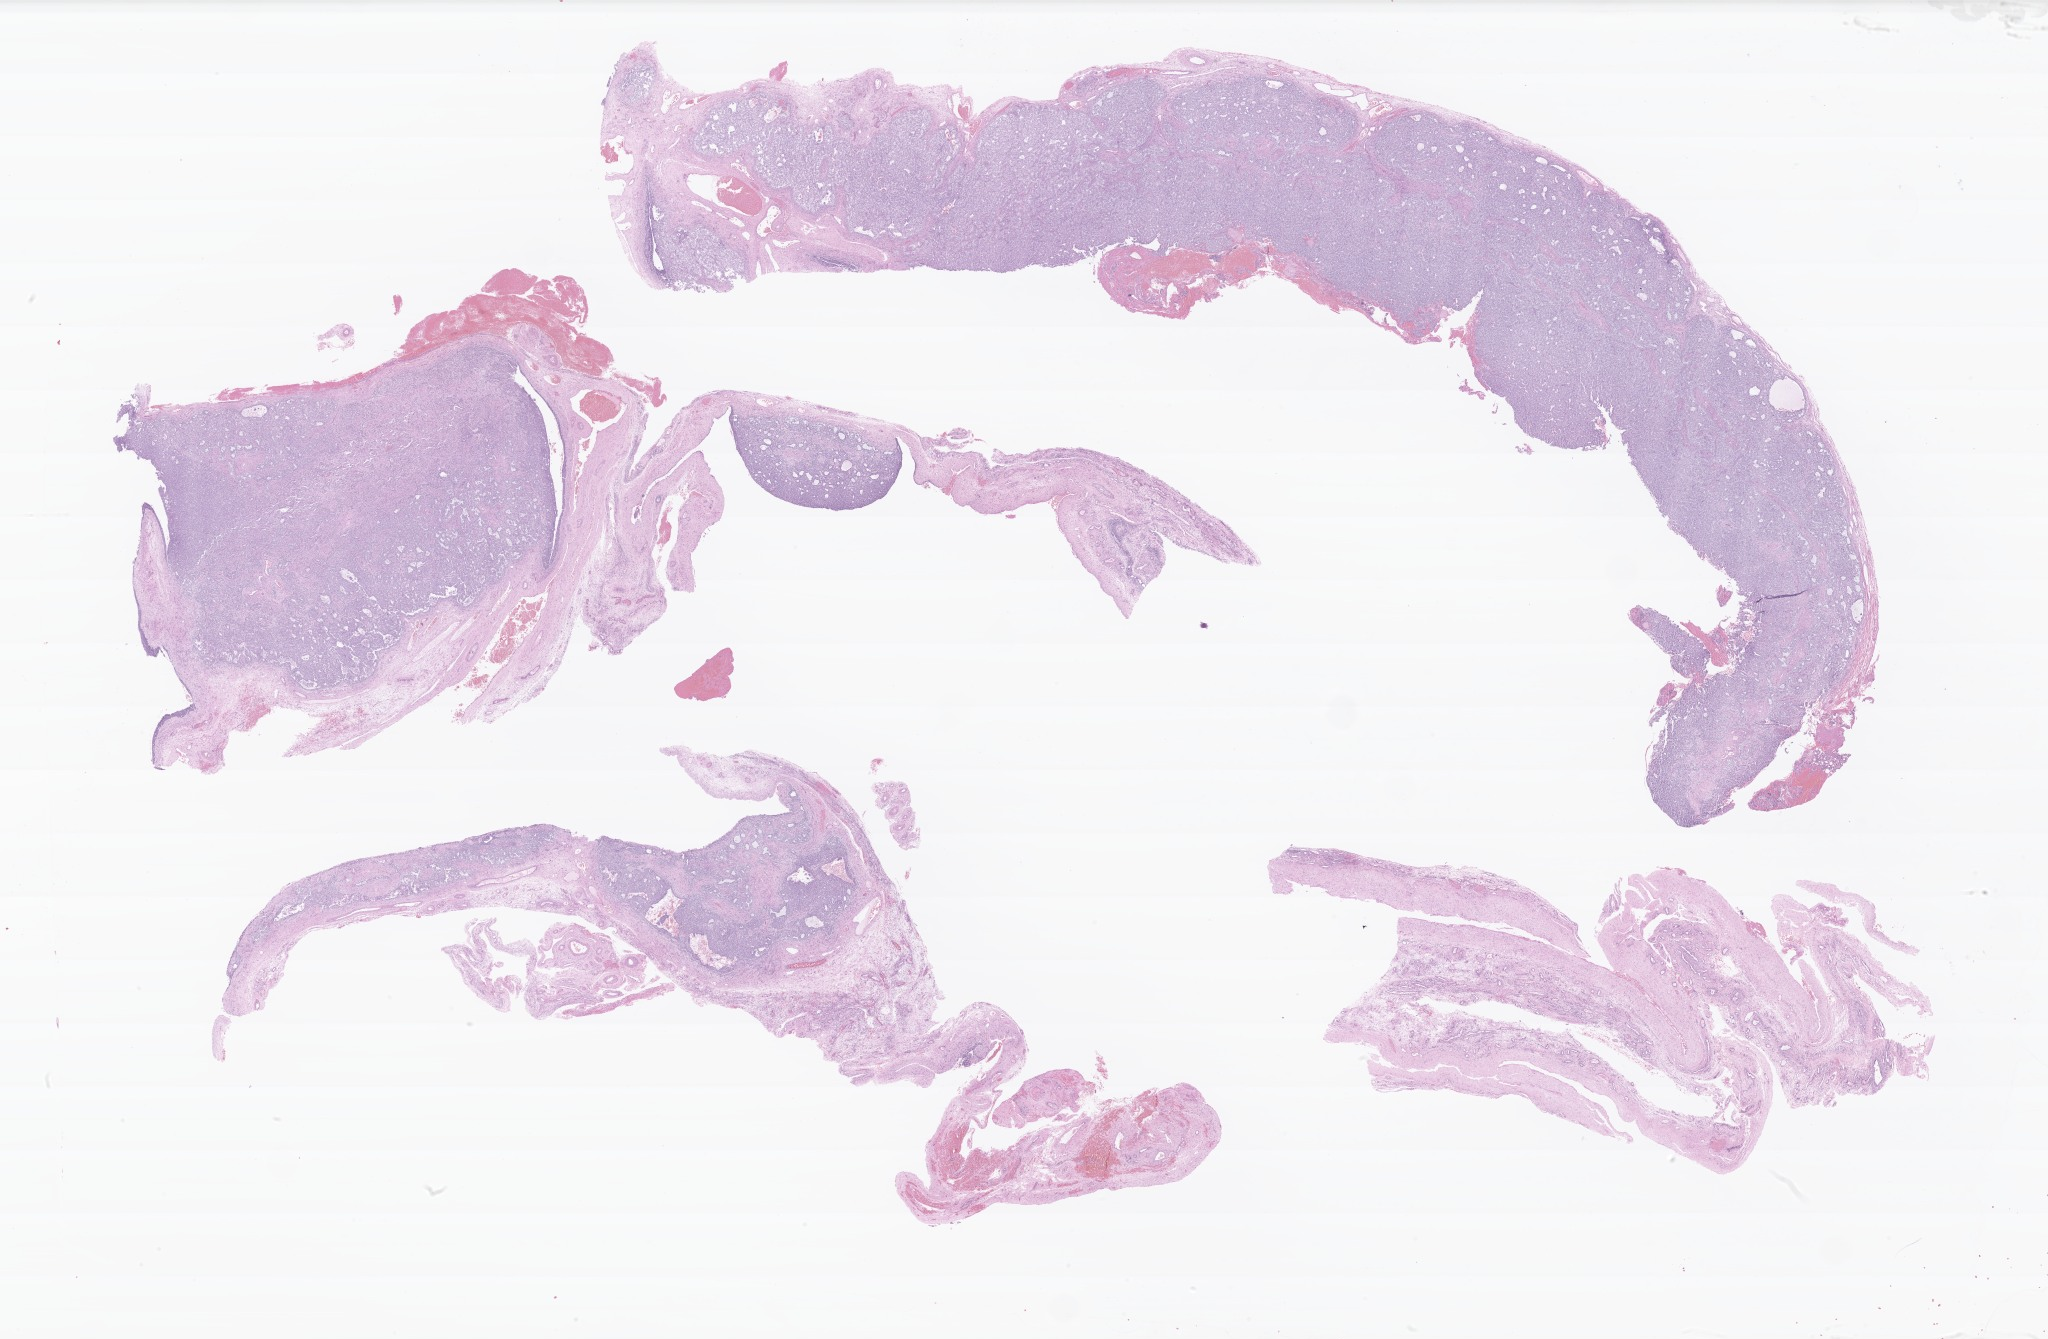
Digitized hematoxylin and eosin (H&E)-stained section of tumor tissue from the ovary, shown as a low-resolution overview of the whole scanned area (about 34.5 x 22.5 mm). Formalin-fixed, paraffin-embedded (FFPE) tissue. Patient: female, age 186 months (15 years 6 months).
- diagnosis: Granulosa cell tumor, juvenile